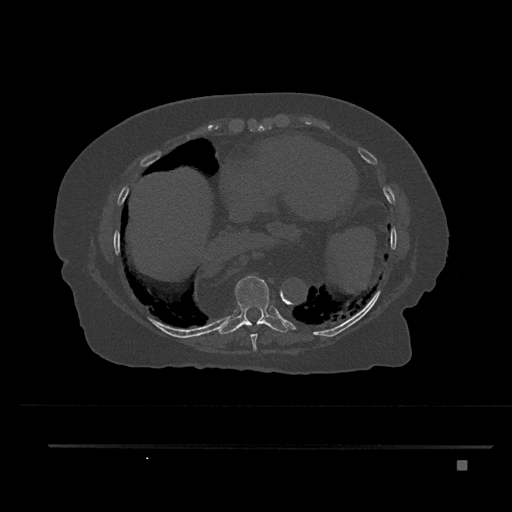
CT including the spine, one axial slice. Position 411 of 797 along the scan axis. 120 kVp. Bone window (W 1800 / L 400 HU). 0.5 mm slice thickness. 512 × 512 image matrix, field of view 437 × 437 mm. Patient: female, 76 years. Case-level facts recorded for this patient, not image findings: primary cancer: lung; vertebrae with lytic lesions (as recorded): T11, L3.
Structures marked on this image (semi-automatic segmentation, software-assisted and operator-edited):
- T8 vertebra: bounding box (x1, y1, x2, y2) in pixels: (250, 333, 257, 351)
- T9 vertebra: (217, 276, 289, 335)